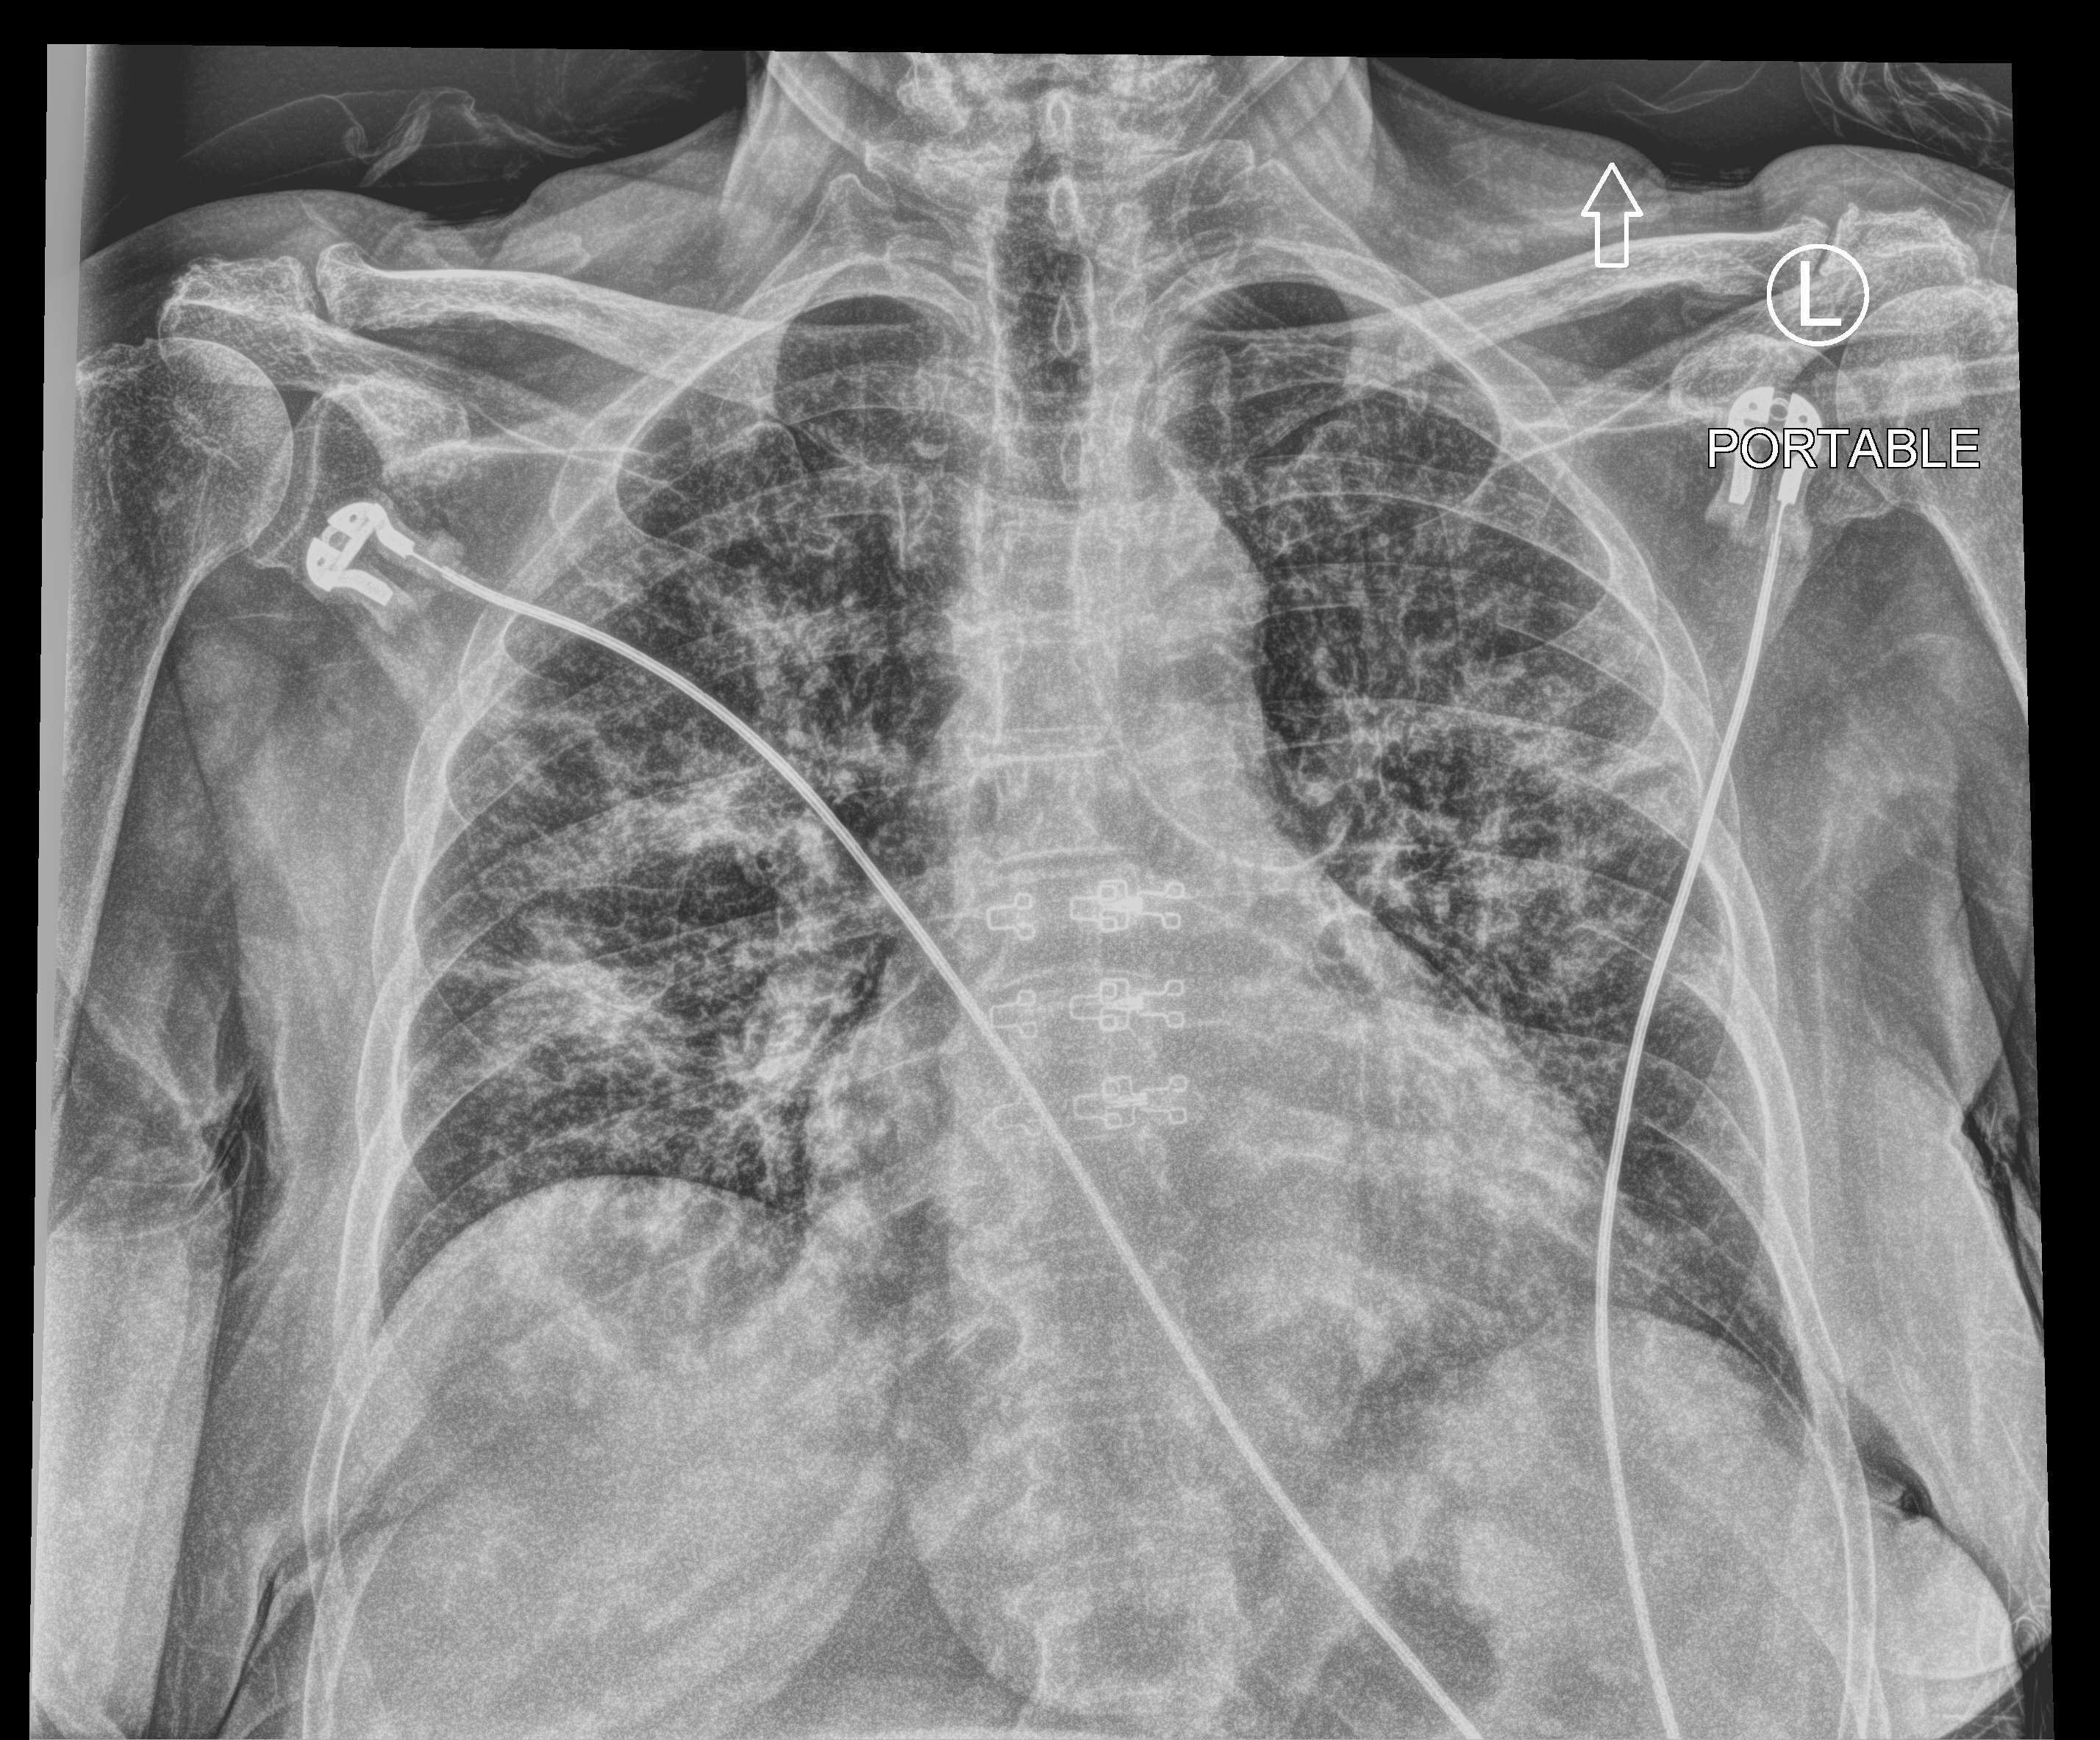
Portable chest radiograph, anteroposterior (AP) projection. Female patient hospitalised with COVID-19, age 60–74 years.
Admission-level facts for this patient (not findings on this image; timing relative to this image not recorded): hypertension (admission record): no; admitted to intensive care during this hospital stay: no.